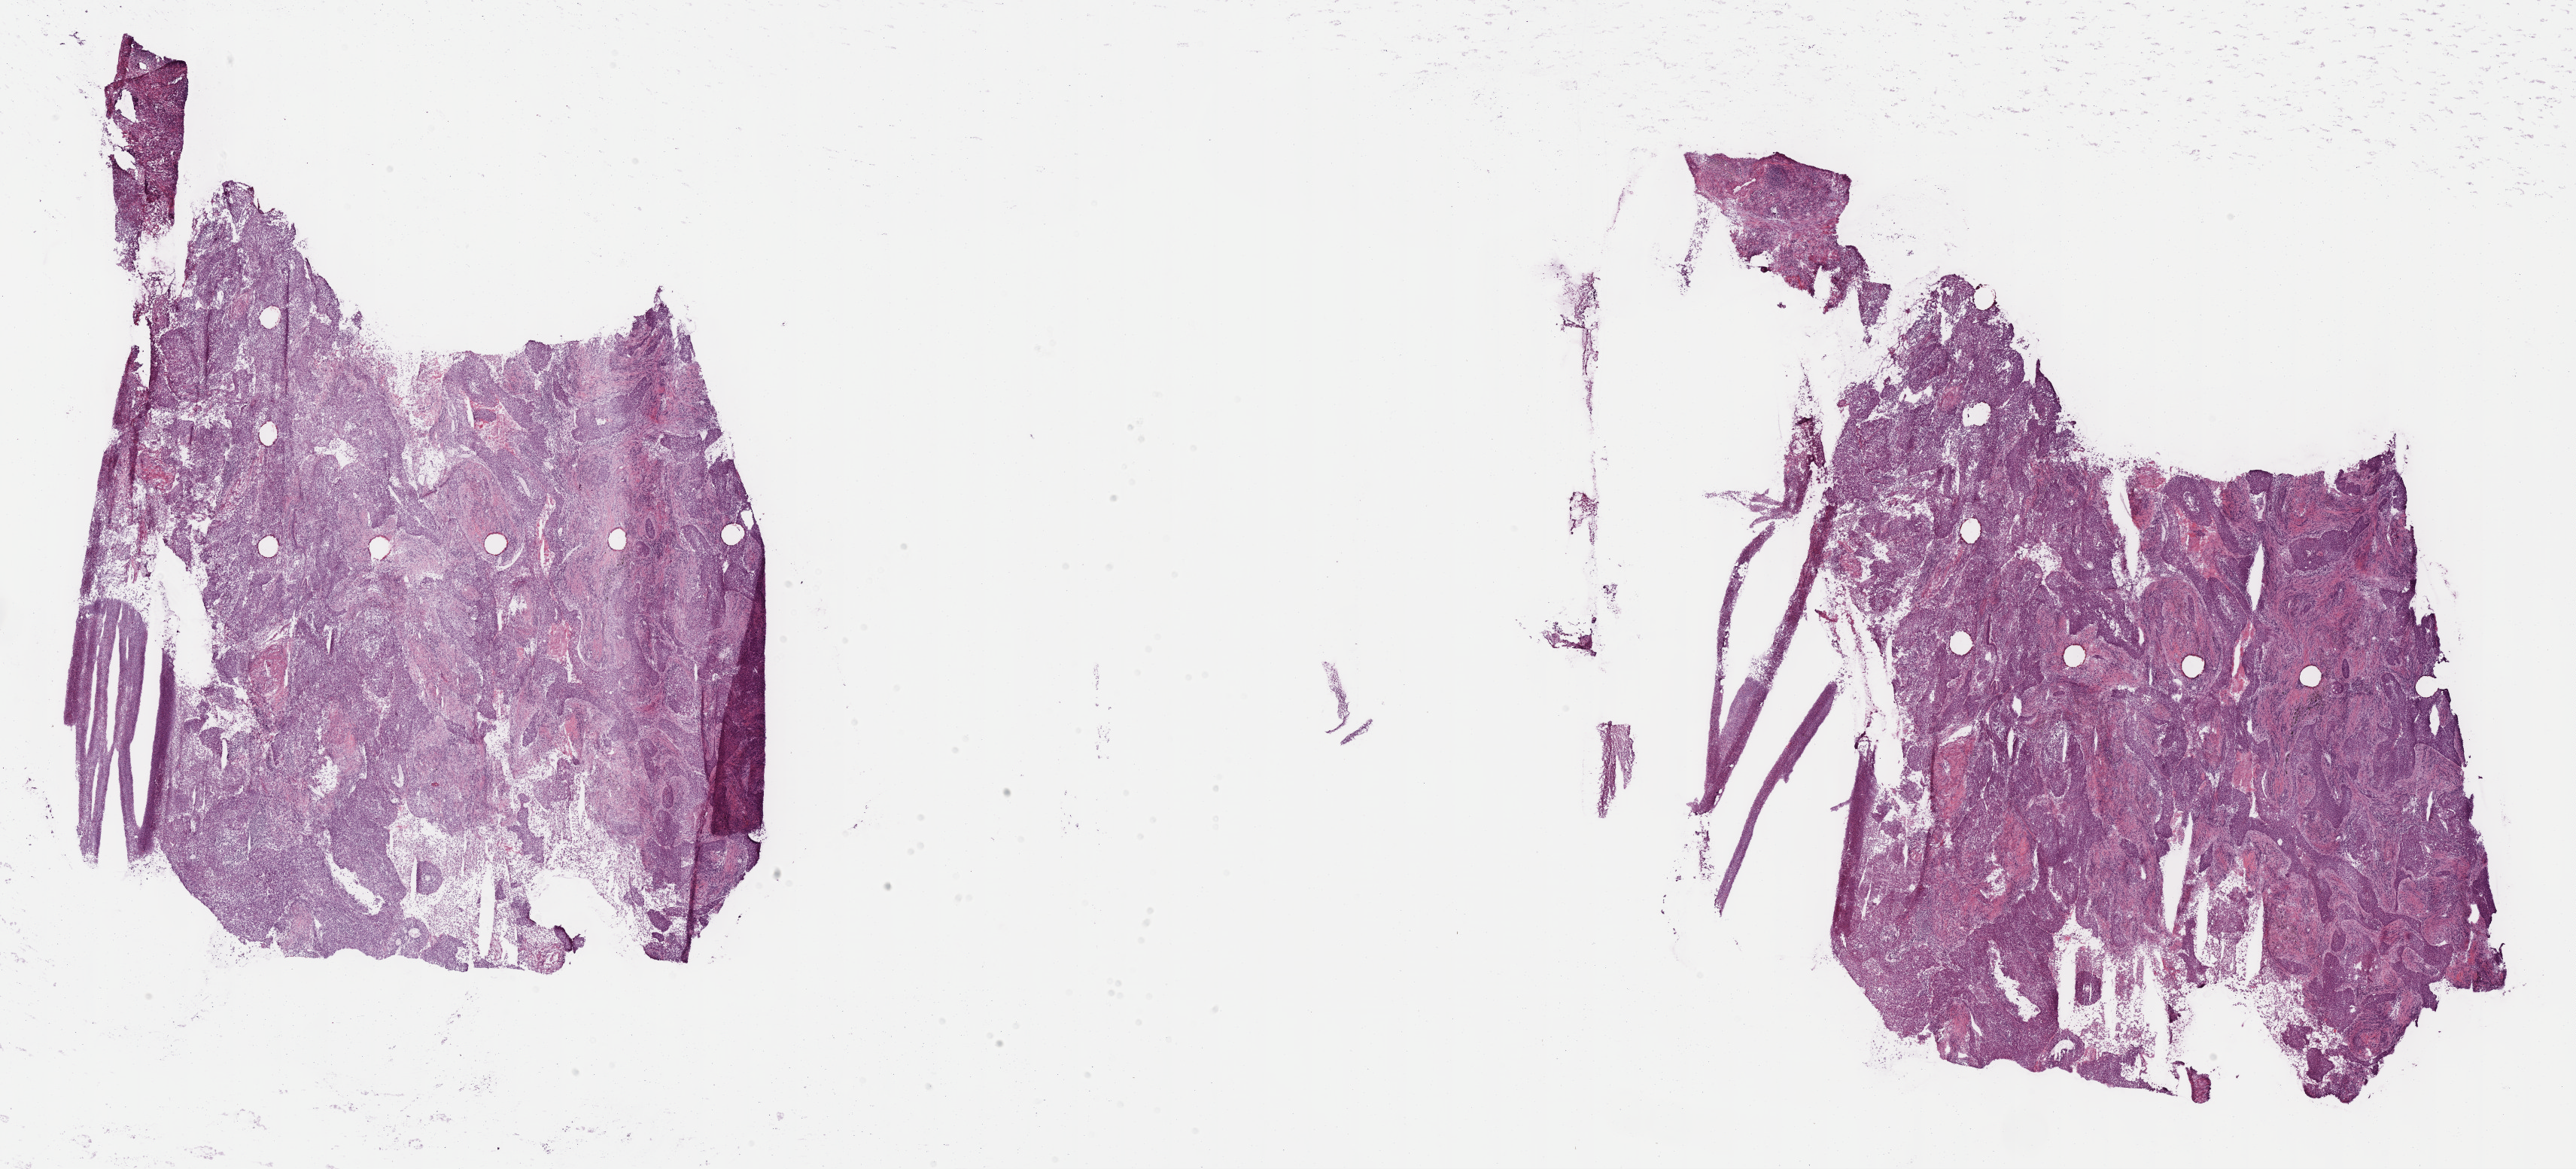
Digitized H&E tissue section (whole slide), whole scanned area (about 27.7 x 12.6 mm) shown as a low-resolution overview; frozen section from the top of the tissue portion; sample: primary tumour, lung. Patient: male, age at initial diagnosis 70 years. Pathologist review of this section (percent, as recorded): tumour cells 90%, tumour nuclei 70%, normal cells 0%, stromal cells 0%, necrosis 10%. Inflammatory infiltration, as recorded: lymphocyte infiltration 25%, monocyte infiltration 0%, neutrophil infiltration 0%.
• histologic diagnosis: Squamous cell carcinoma, NOS
• TNM: T3 N1 M0
• AJCC pathologic stage: IIIA
• laterality: right